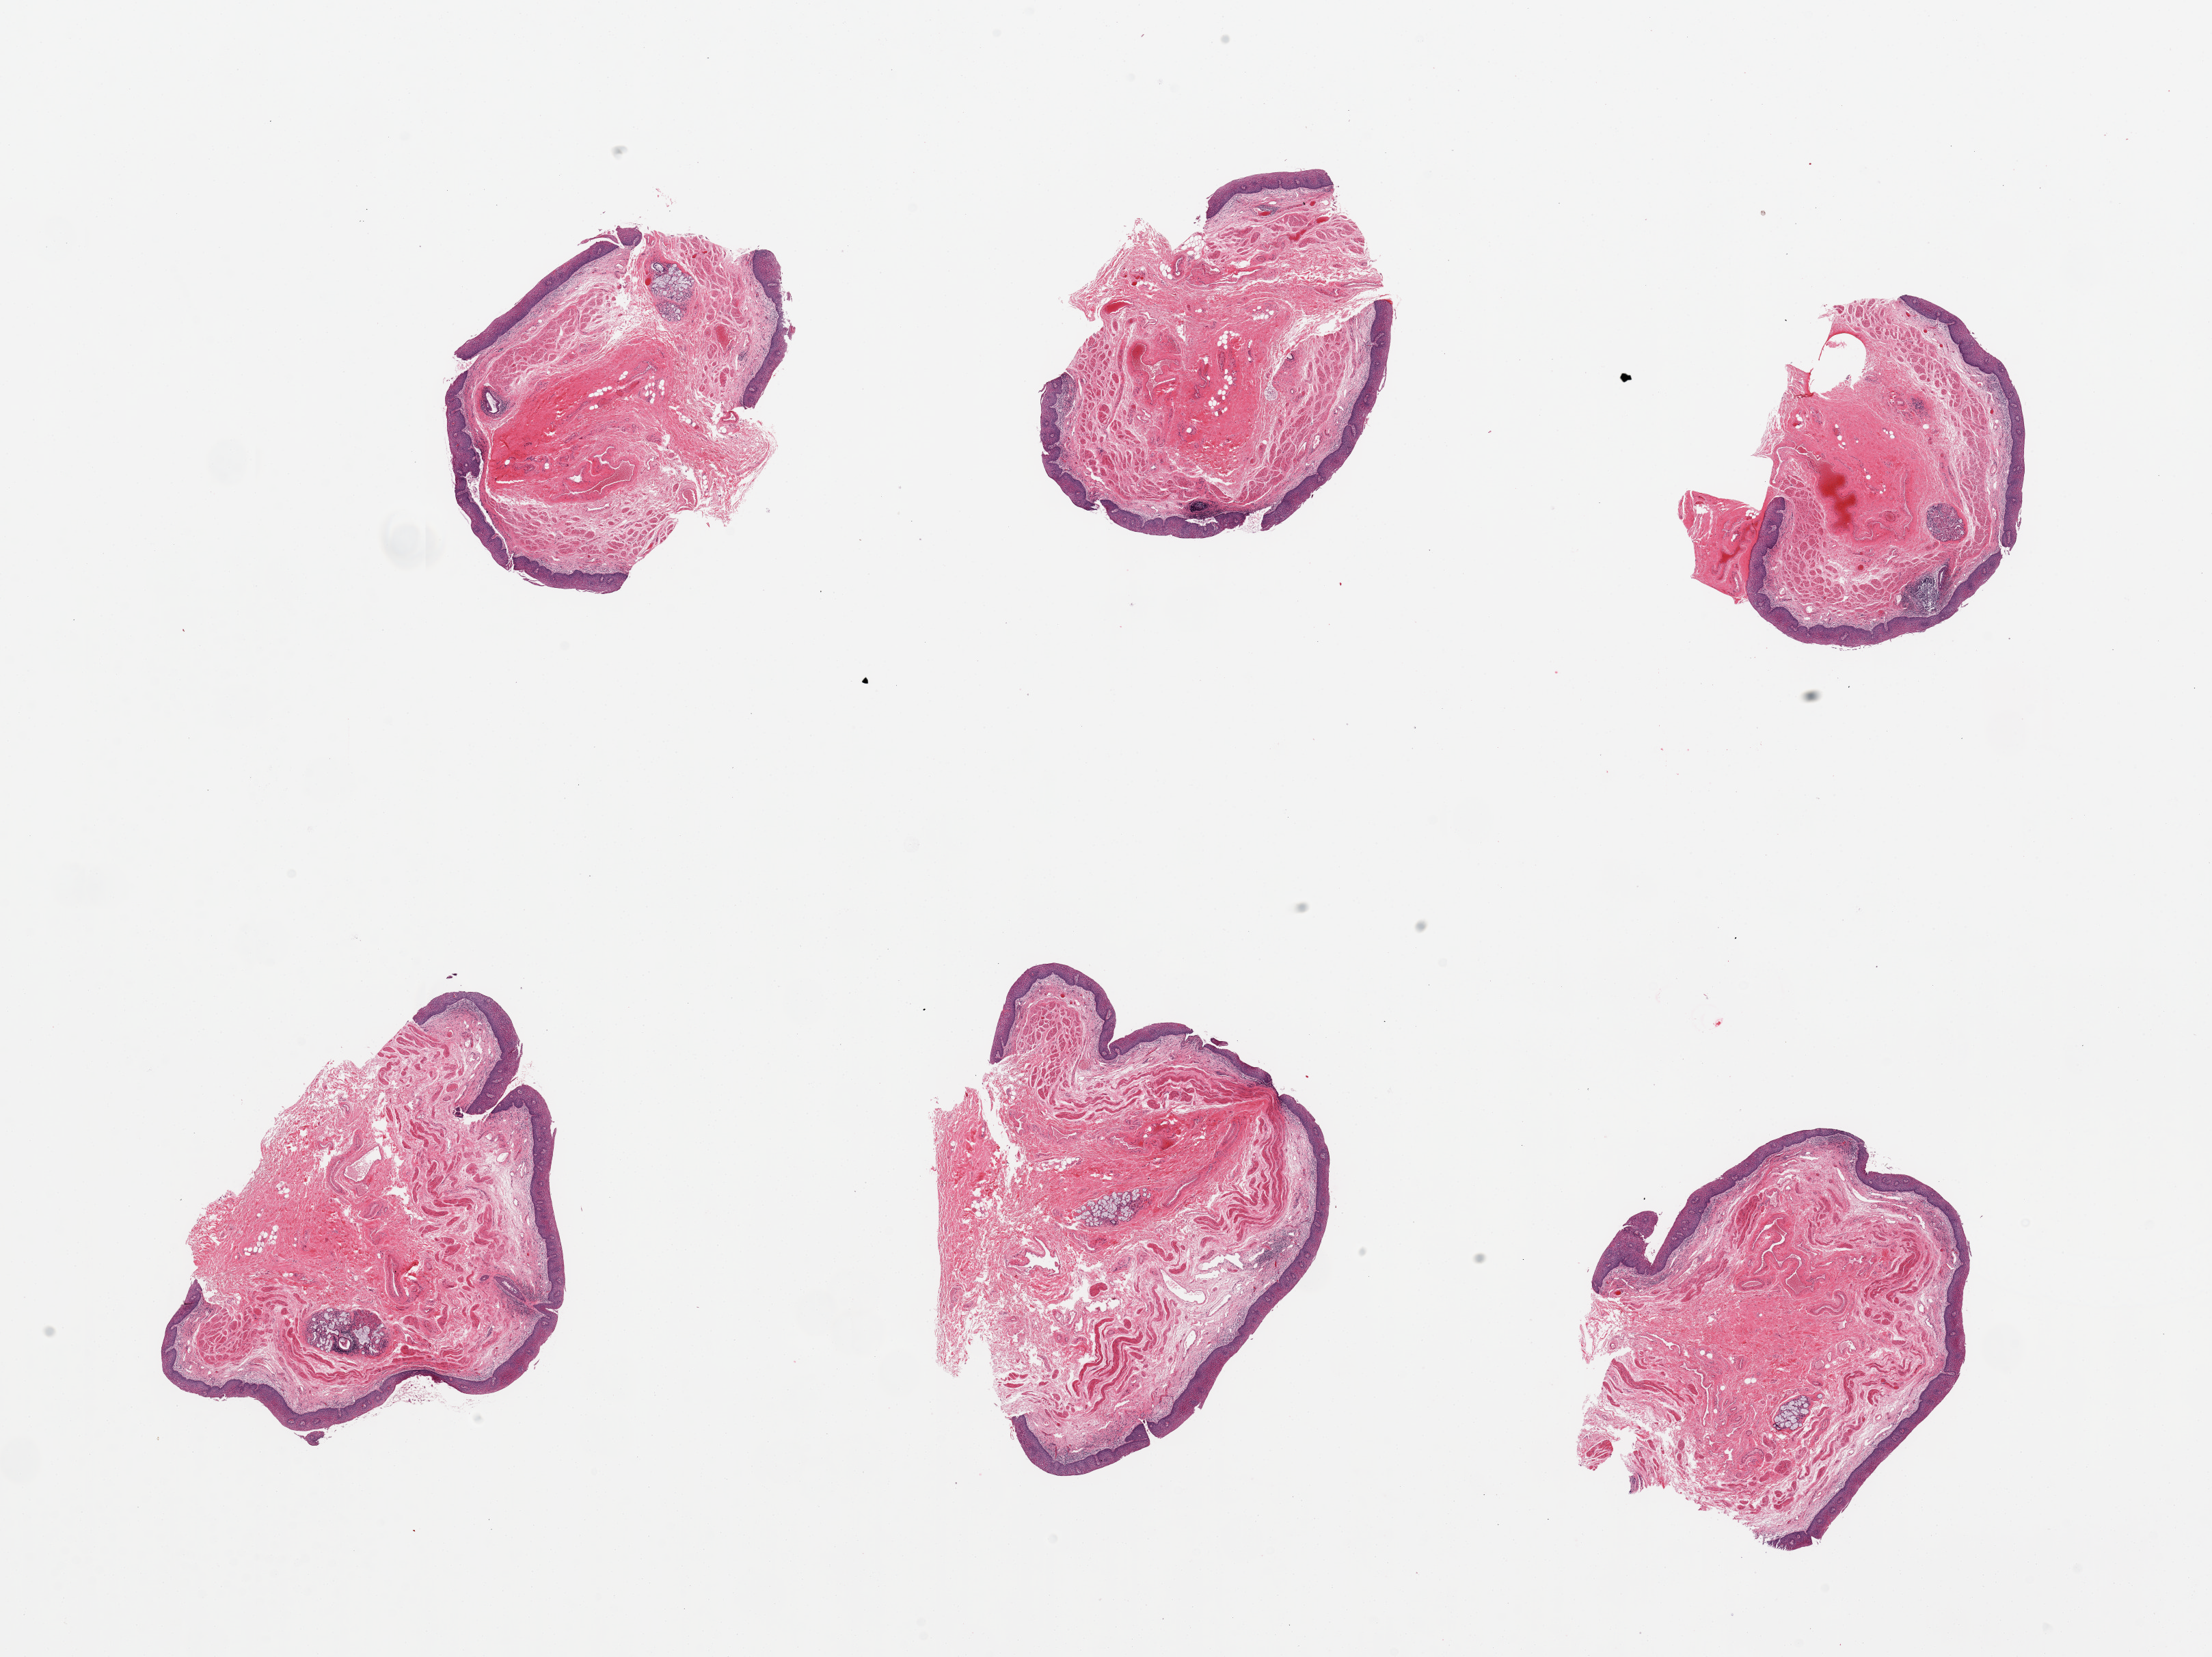
H&E whole-slide image, a low-resolution overview of the entire scanned area, about 25.6 x 19.2 mm. PAXgene-fixed, paraffin-embedded tissue. Target tissue: esophageal mucous membrane. Tissue donor sample. Male donor.
Pathologist's review note for this sample: 6 pieces, squamous mucosa is ~0.2mm, ~10% thickness; submucosal mucus glands present.